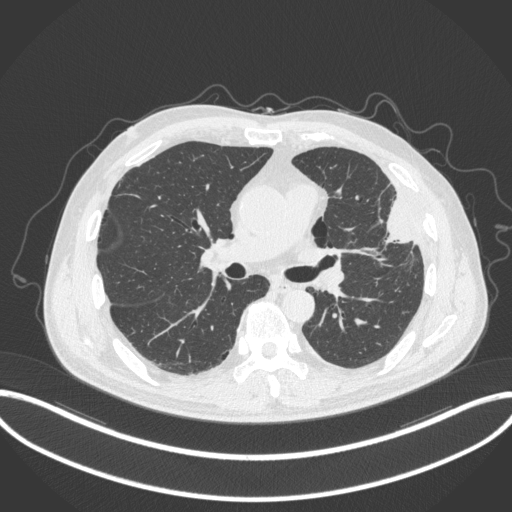
Chest CT, one axial slice. Position 190 of 382 along the scan axis. 120 kVp. Lung window (W 1500 / L -600 HU). 1 mm slice thickness. 512 × 512 image matrix. Male patient, age 64 years. Case-level facts recorded for this patient, not image findings: clinical TNM (as recorded): T4 N1 M0; histopathological grade: G3.
Outlined on this slice (bounding box drawn by a radiologist):
- lung tumour (recorded histology: adenocarcinoma): box from (x=376, y=193) to (x=421, y=248) px